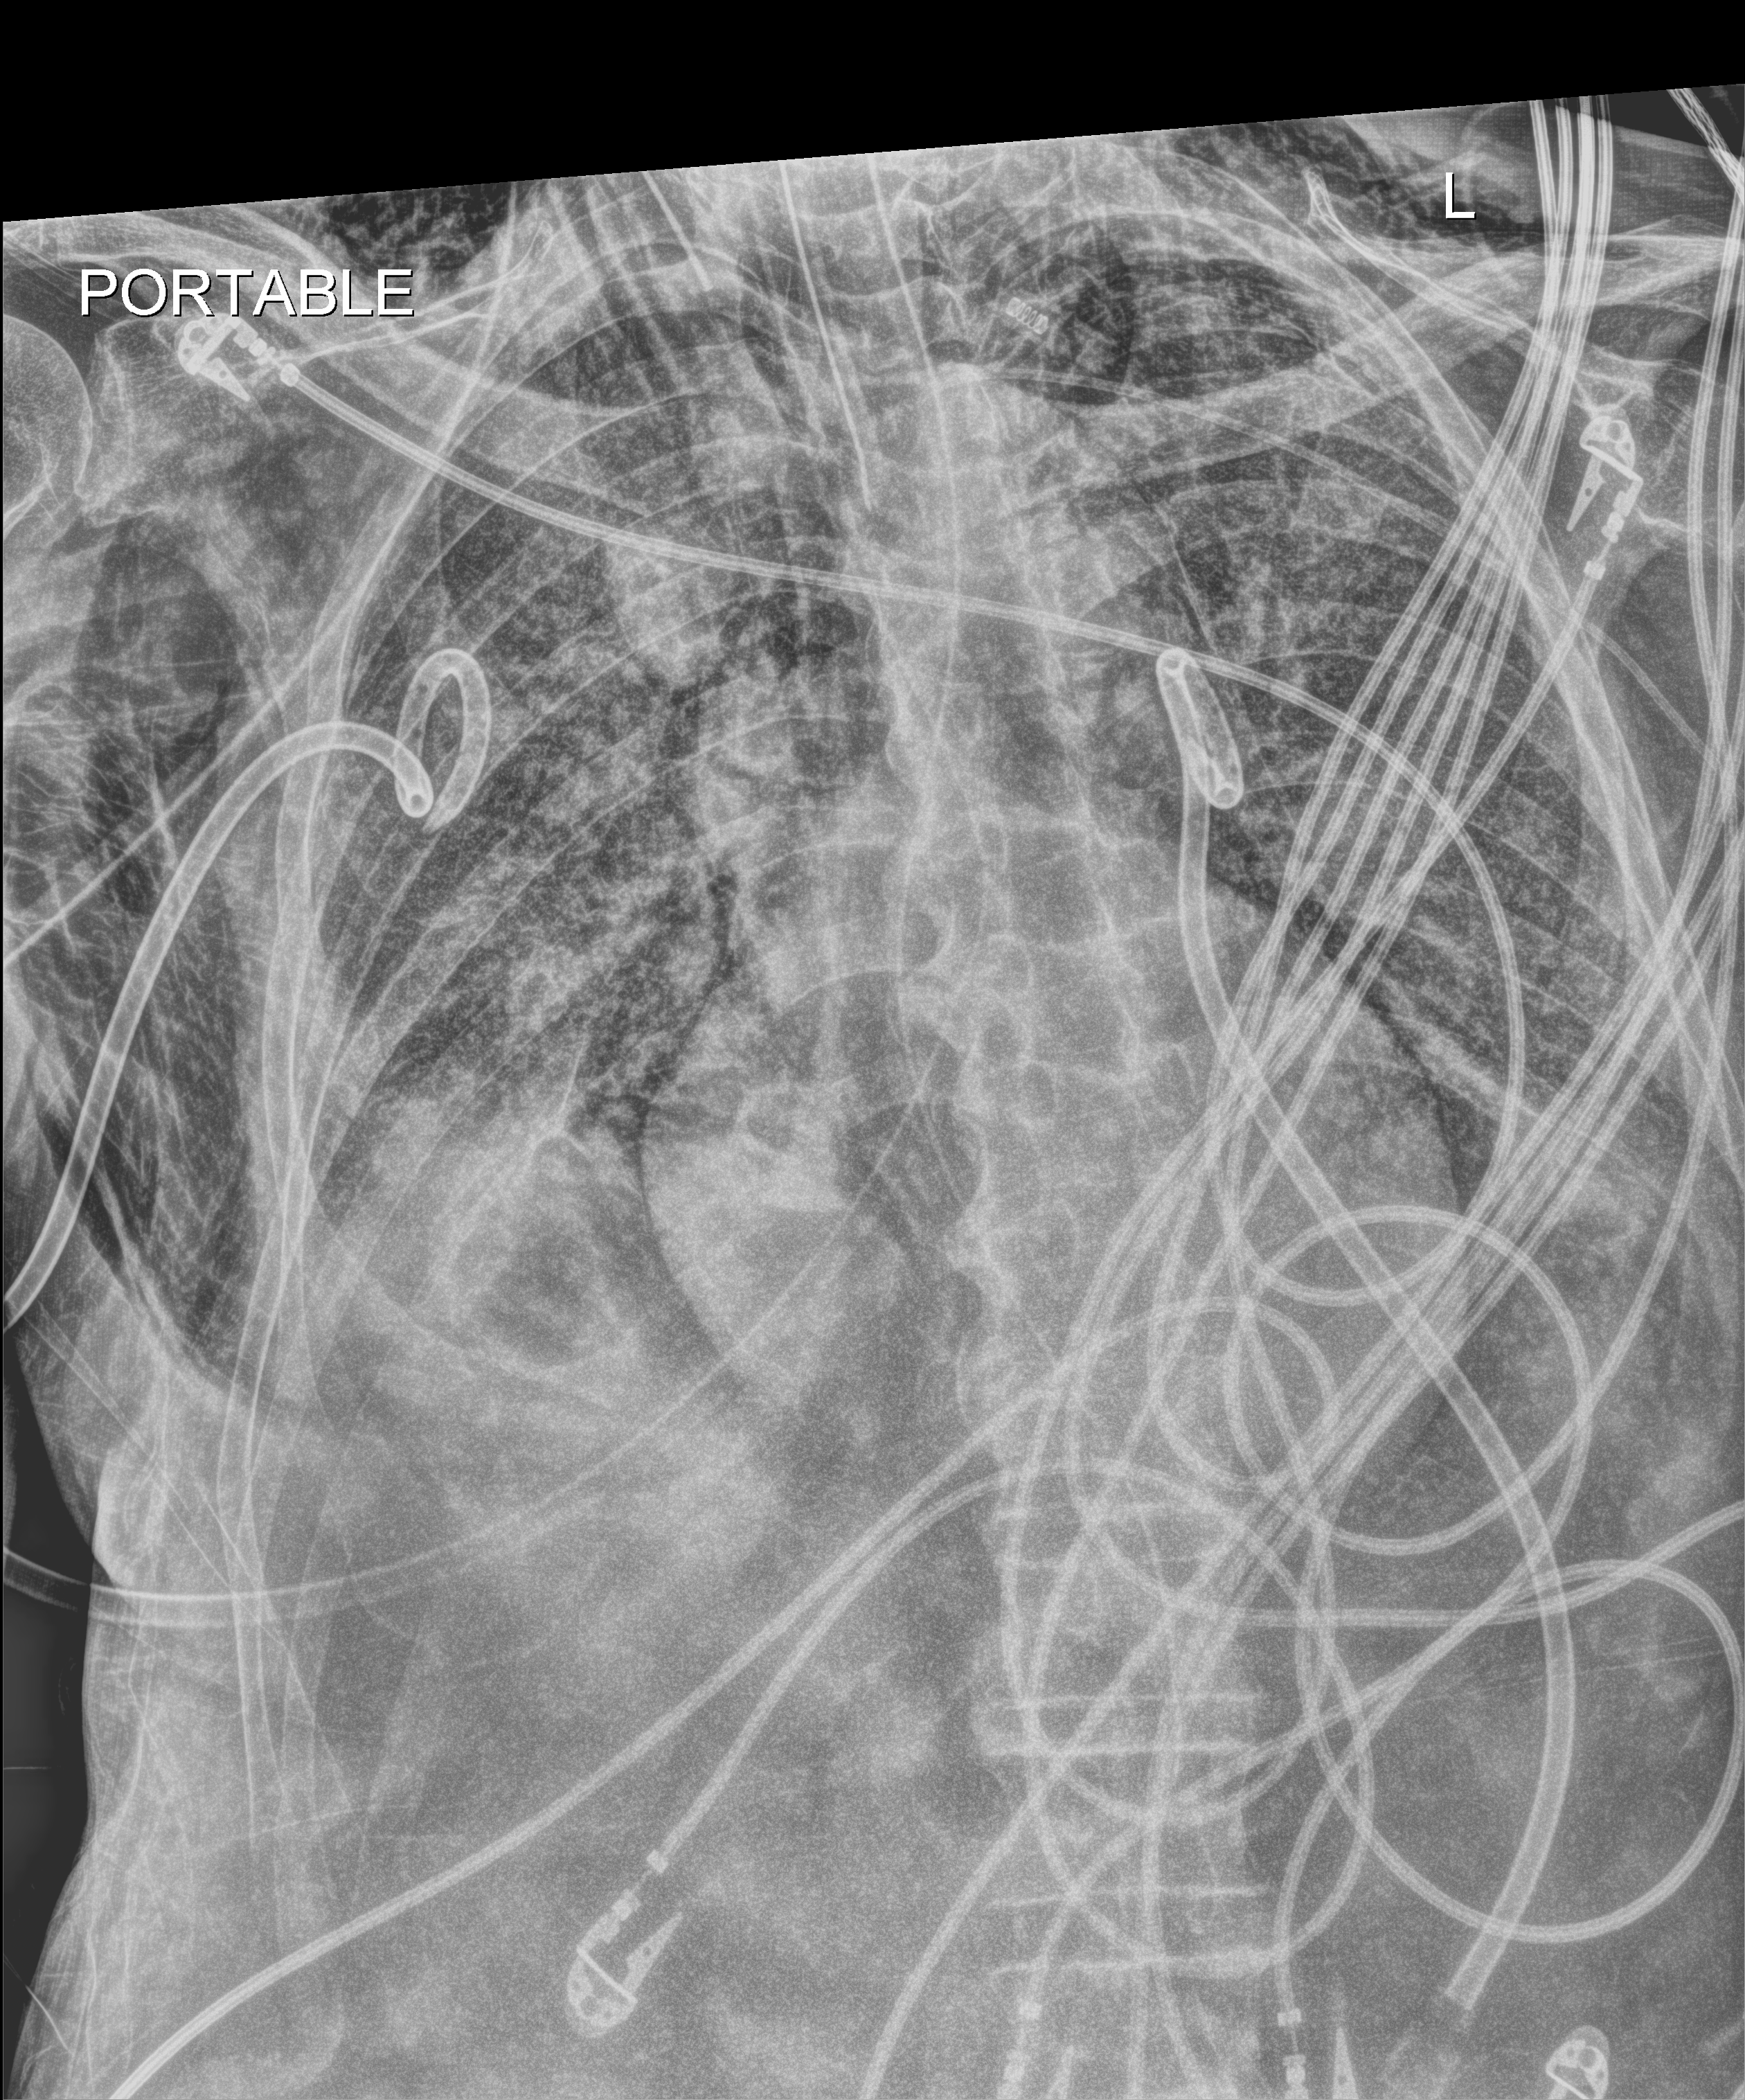
Portable chest radiograph, anteroposterior (AP) projection. Male patient hospitalised with COVID-19, age 75–90 years.
Admission-level facts for this patient (not findings on this image; timing relative to this image not recorded): mechanically ventilated during this hospital stay: yes.